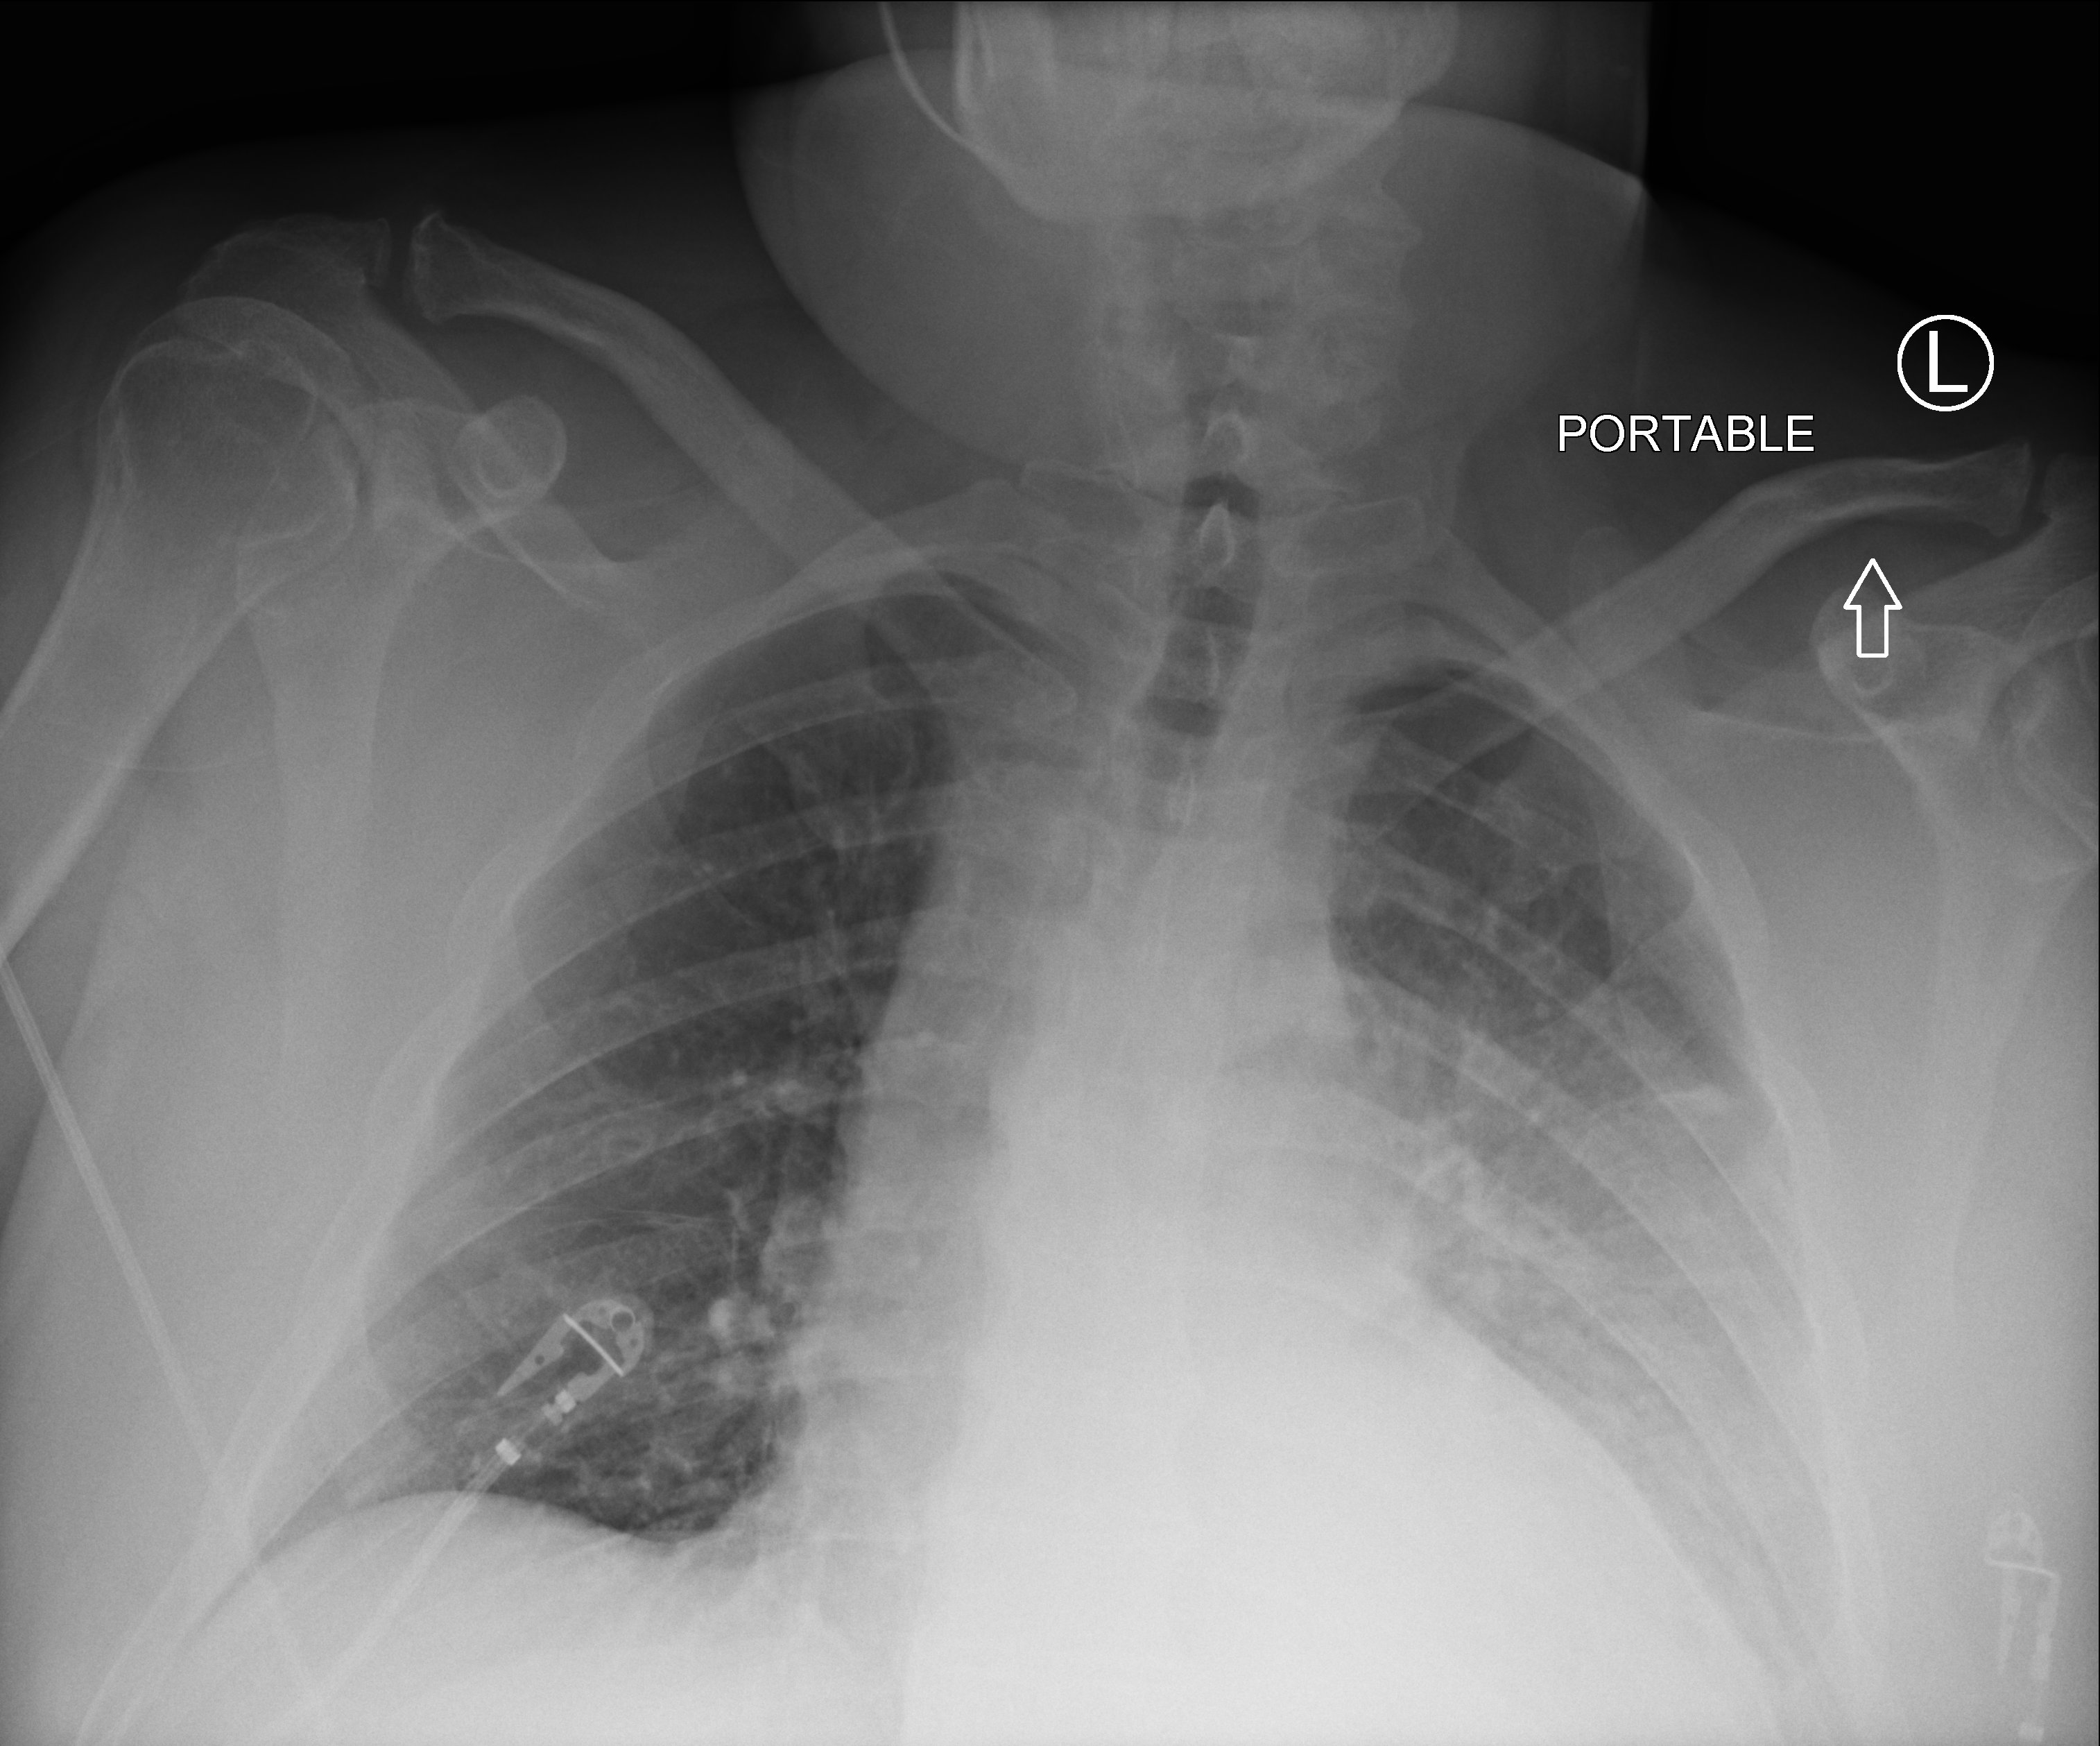
Portable chest radiograph, anteroposterior (AP) projection. Male patient hospitalised with COVID-19, age 18–59 years.
Hospital-stay facts (about this admission, not read from this image; timing relative to this image not recorded):
- mechanically ventilated during this hospital stay: no